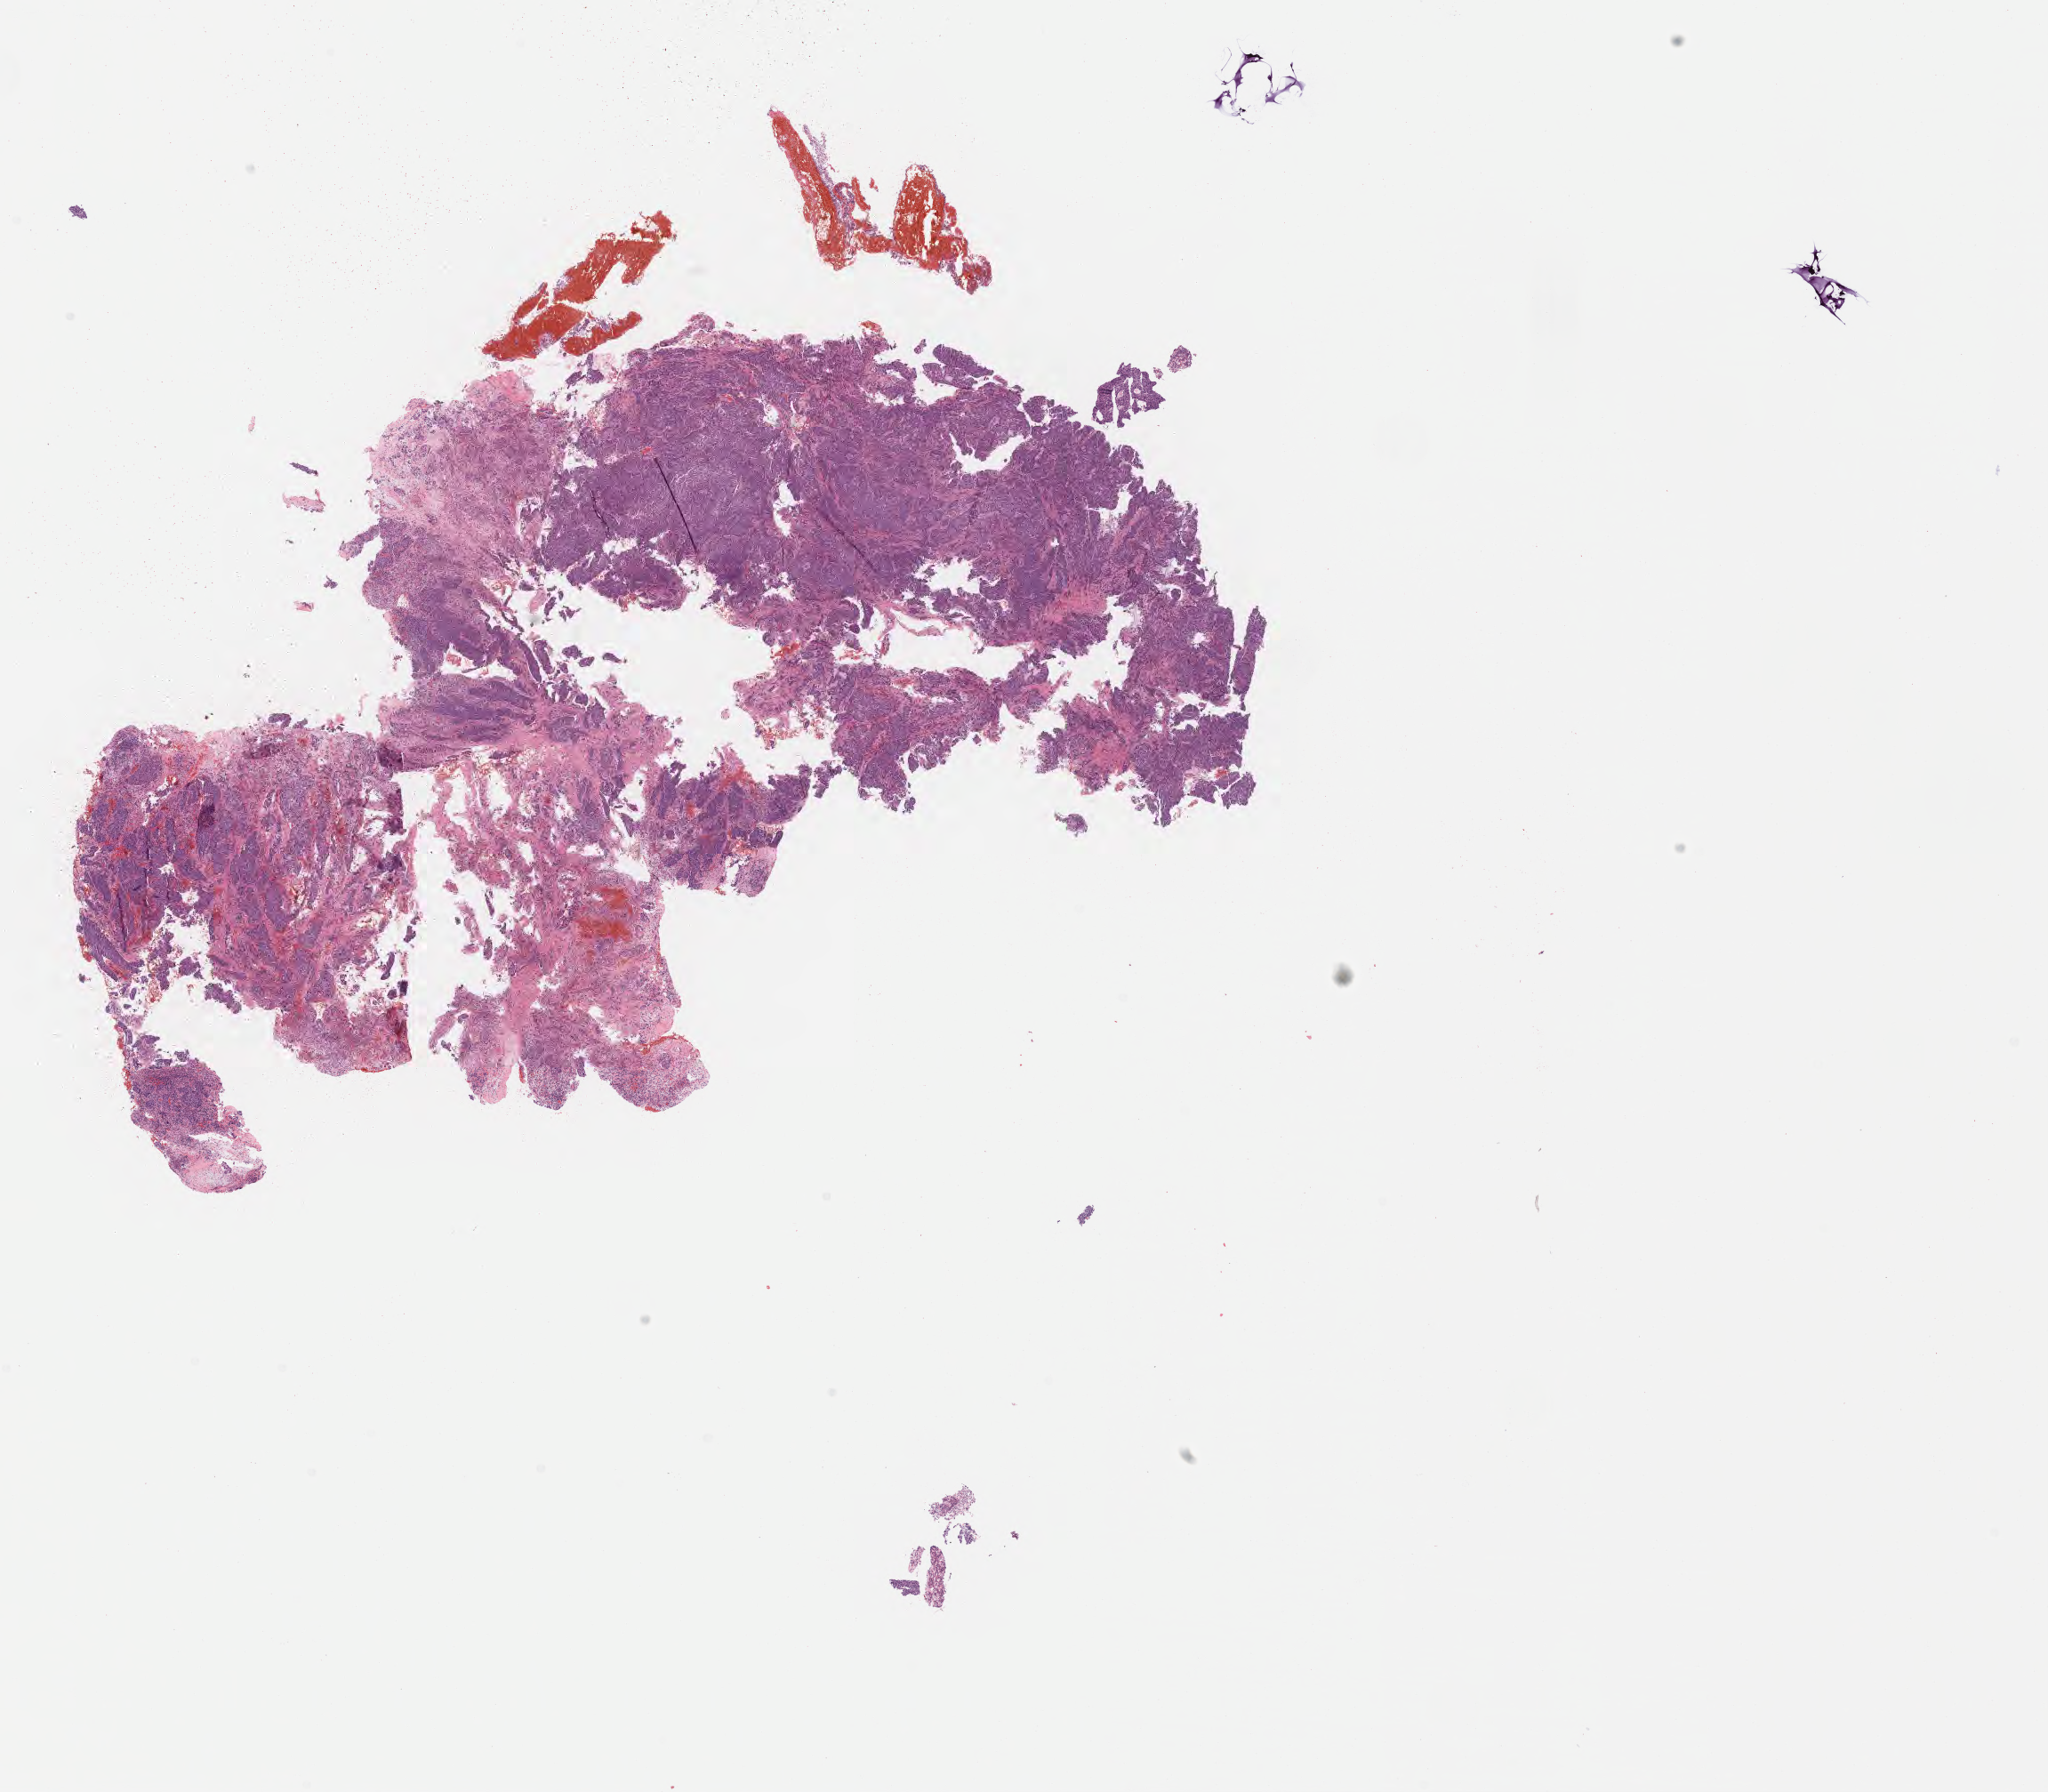
Haematoxylin and eosin whole-slide image — a low-resolution overview of the entire scanned area, about 18.6 x 16.3 mm, tumor tissue, site: cervix. Patient: female, 46 years old.
• diagnosis: Squamous cell carcinoma, large cell, nonkeratinizing, NOS